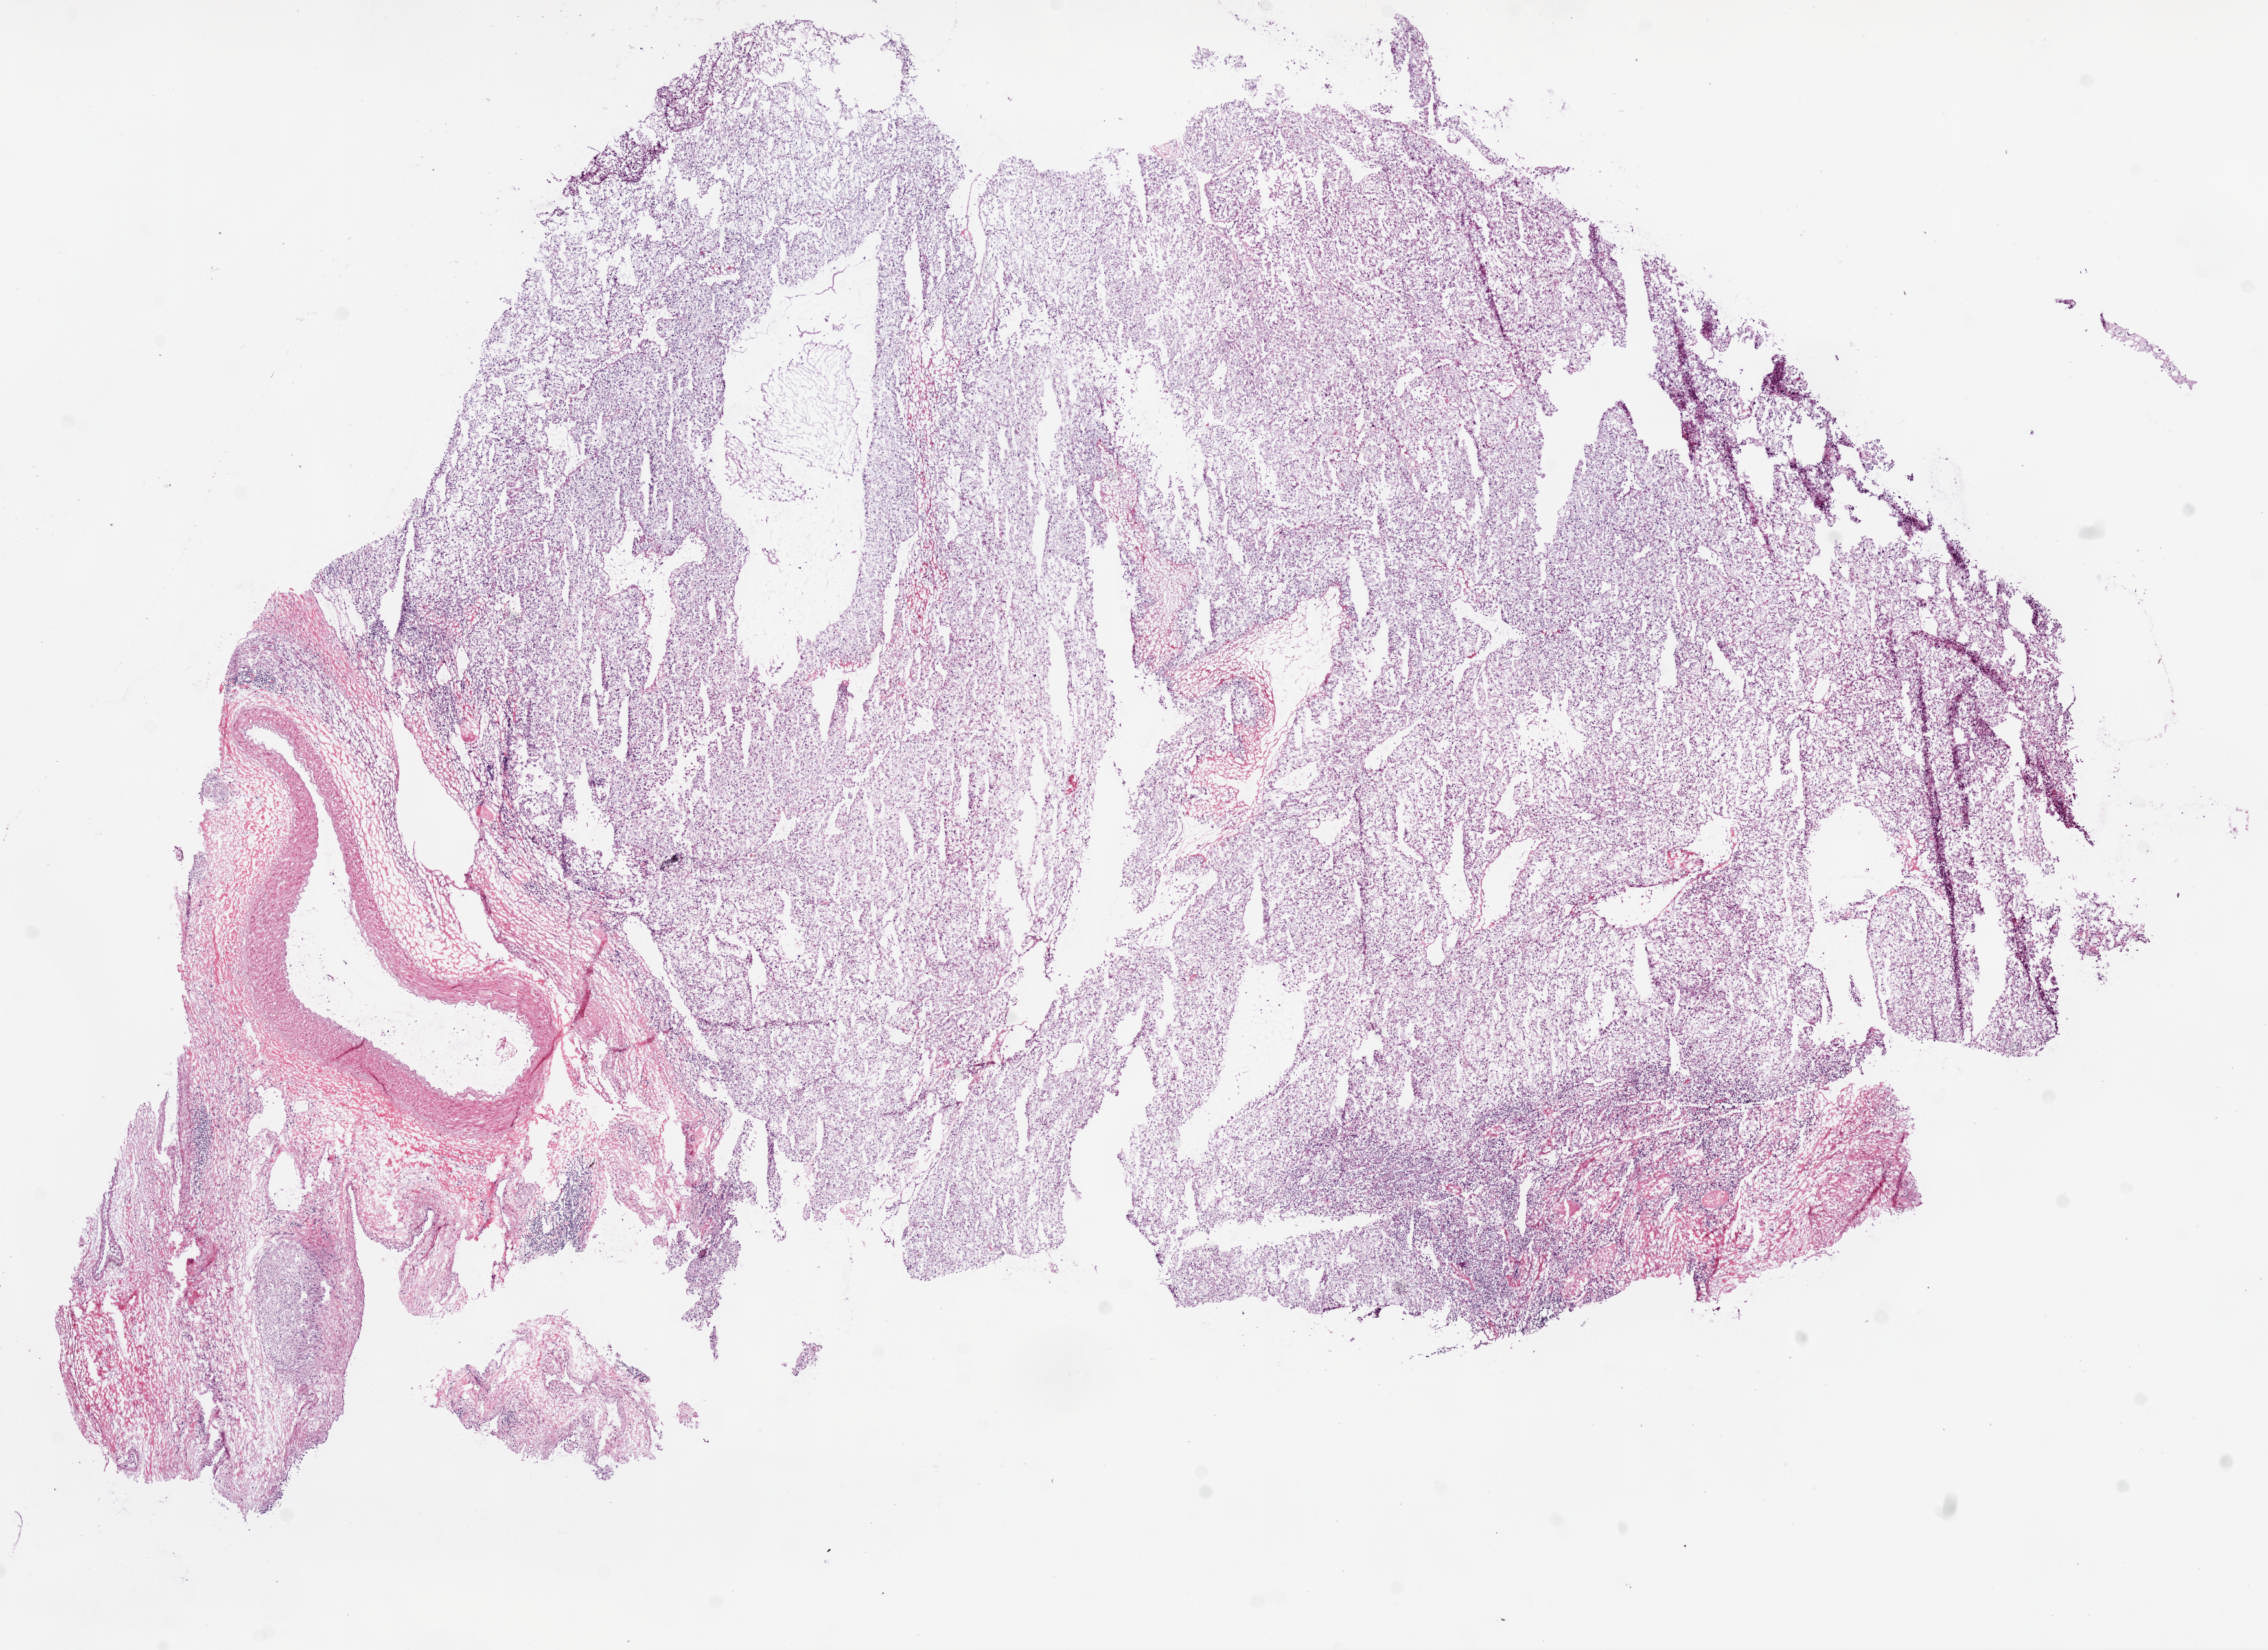
H&E whole-slide image — a low-resolution overview of the entire scanned area, about 14.0 x 10.2 mm (from a 20x scan). Frozen section from the top of the tissue portion. Primary tumour sample from the kidney. Patient: male, age at initial diagnosis 61 years. Histologic grade: G3 (poorly differentiated). Pathologist review of this section (percent, as recorded): tumour cells 80%, tumour nuclei 80%, normal cells 0%, stromal cells 20%, necrosis 0%.
Histologic diagnosis: Clear cell adenocarcinoma, NOS. Laterality: right. AJCC pathologic stage: IV.